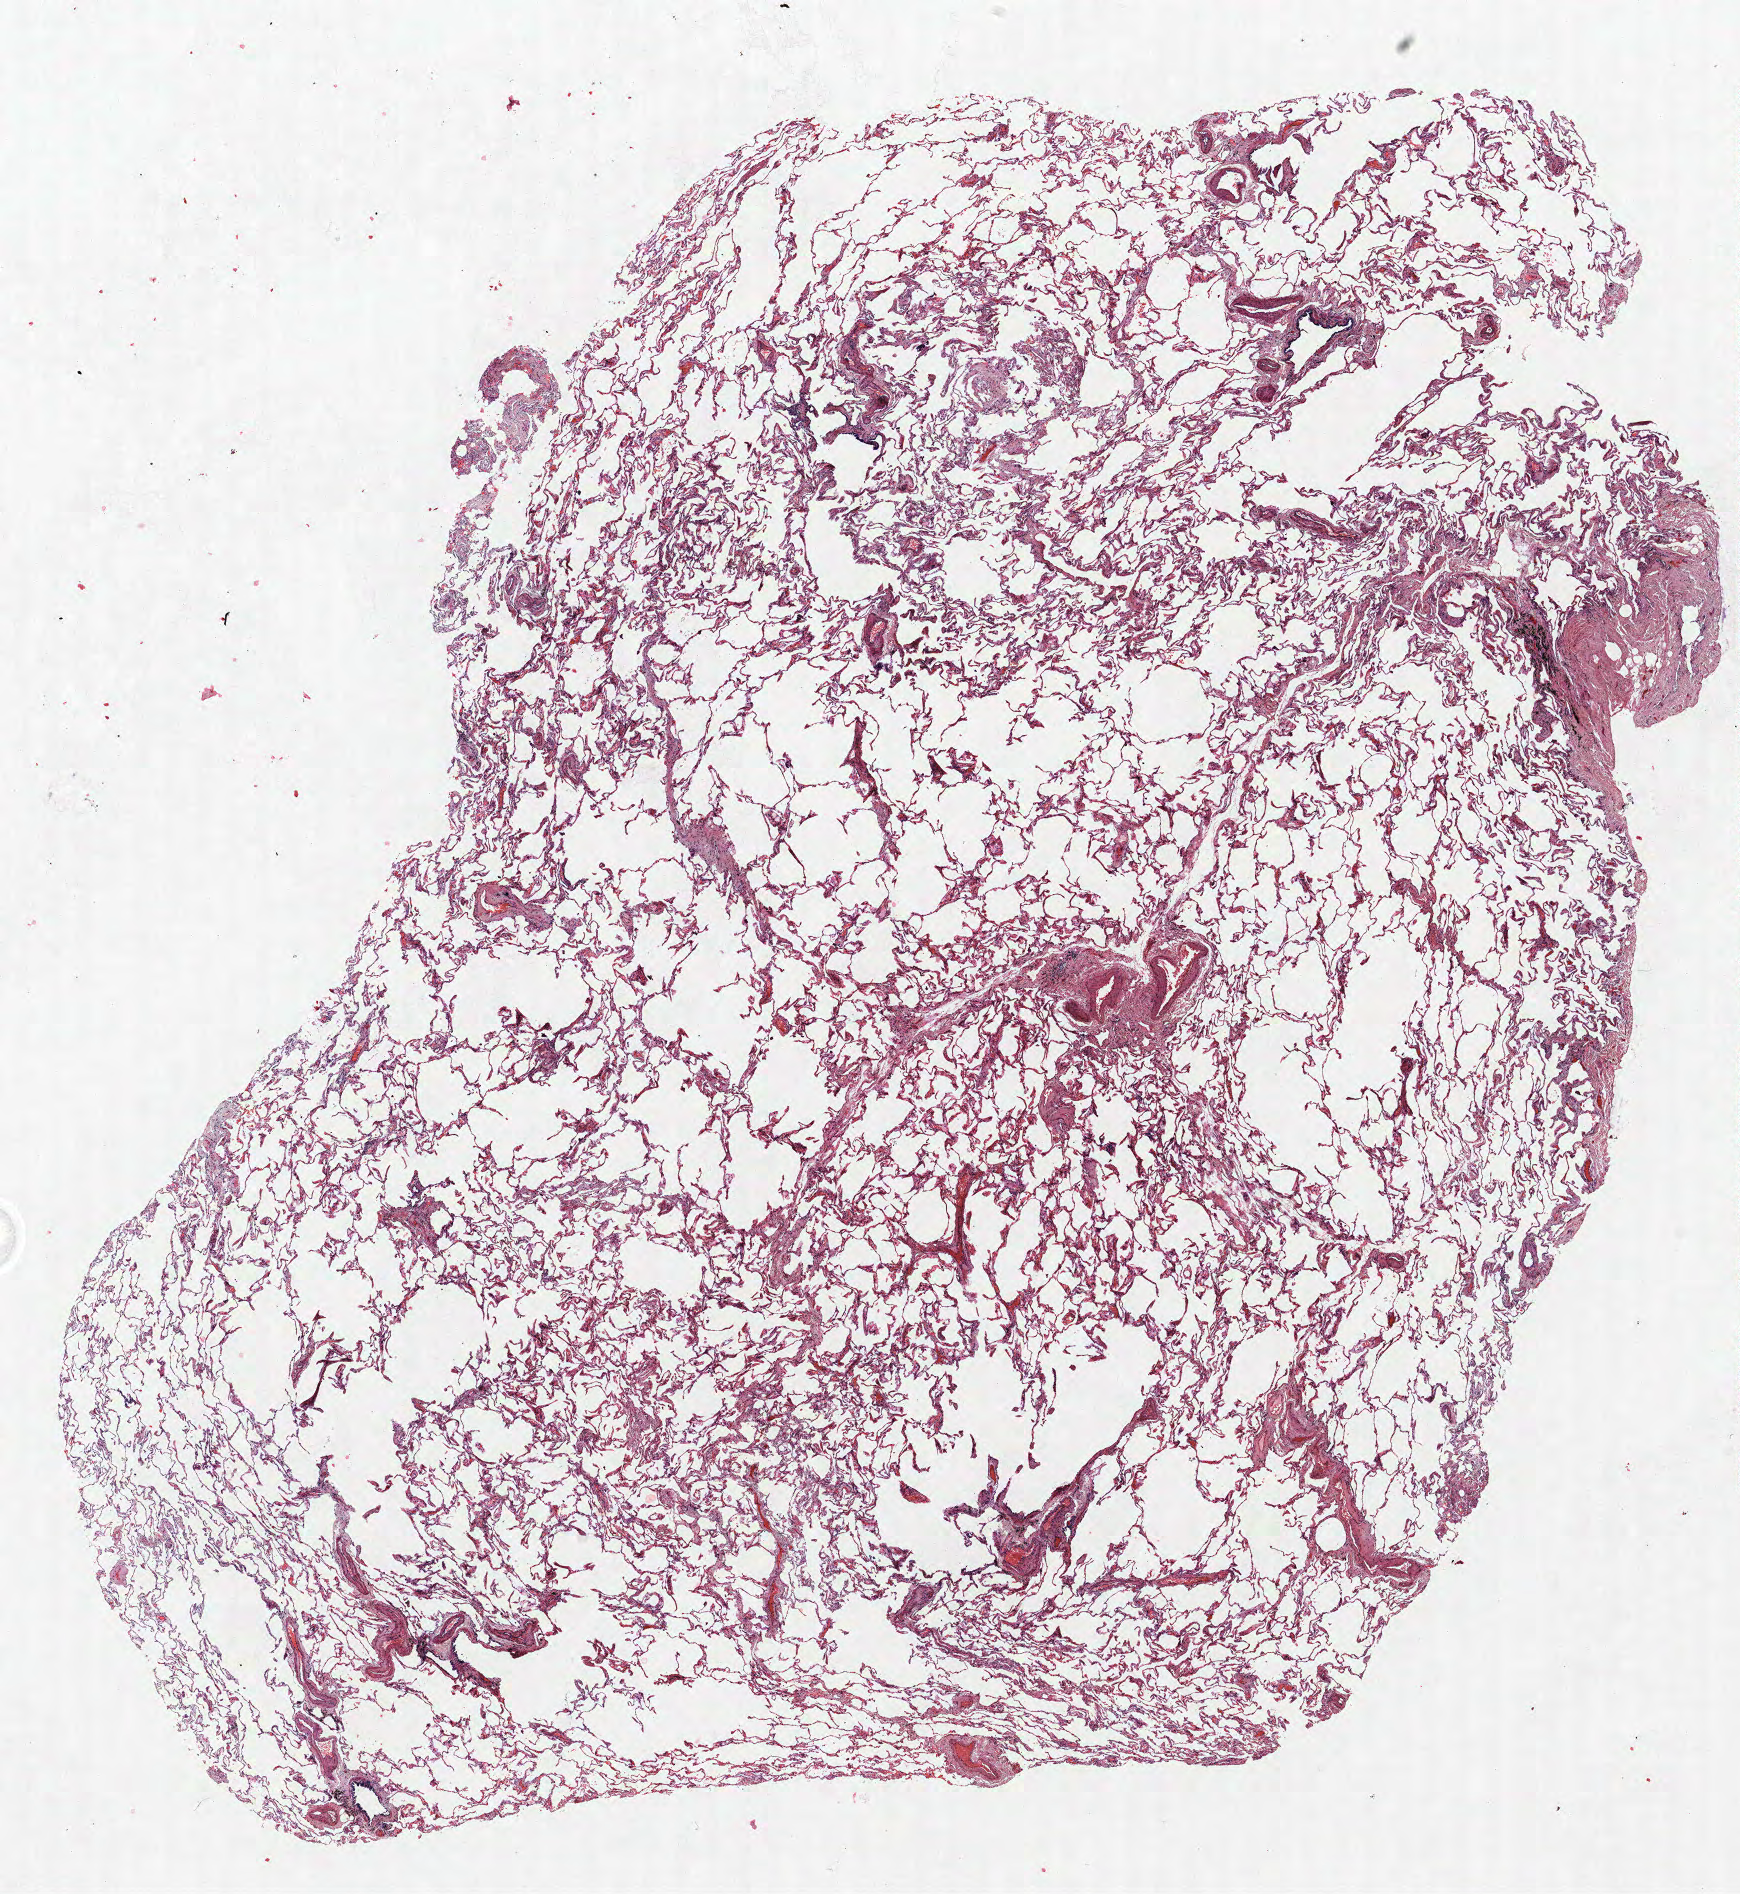
Whole-slide histology image, H&E — low-resolution overview of the scanned area, about 13.9 x 15.2 mm. Formalin-fixed paraffin-embedded (FFPE) section. Lung. Female patient, aged 71 at enrolment. Former smoker at enrolment. Grade: moderately differentiated (G2).
• participant's lung-cancer diagnosis: Adenocarcinoma, NOS
• tumour size (pathology): 12 mm
• primary tumour location (clinical record): left upper lobe
• ICD-O-3 topography: upper lobe of lung (C34.1)
• stage (AJCC 6th edition): IIA